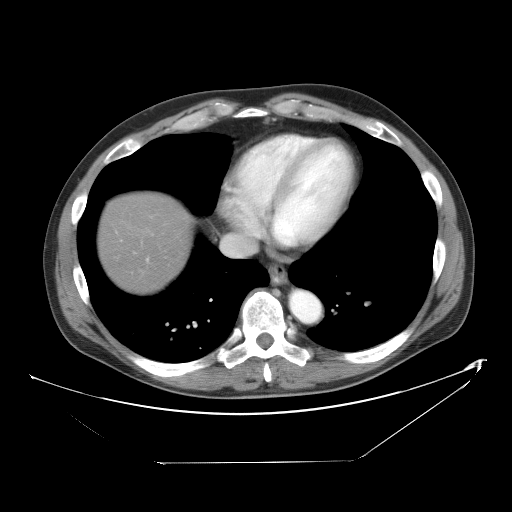
Contrast-enhanced abdominal CT, one axial slice; slice 49 of 53 in the series (ordered by position); reconstruction kernel STANDARD; 120 kVp; intravenous contrast given; soft-tissue window (W 400 / L 40 HU); 5 mm slice thickness; 512 × 512 image matrix, field of view 438 × 438 mm. Male patient, age 59 years. Case-level facts recorded for this patient, not image findings: diagnosis: colorectal cancer liver metastases, imaged before liver resection; multiple liver metastases: yes; largest metastasis: 8.5 cm; chemotherapy before resection: yes.
Annotated regions visible in this slice (outlined manually by an expert reader):
- liver: bounding box (x1, y1, x2, y2) in pixels: (100, 198, 191, 291)
- planned liver remnant (the part of the liver to remain after resection): (100, 198, 190, 292)